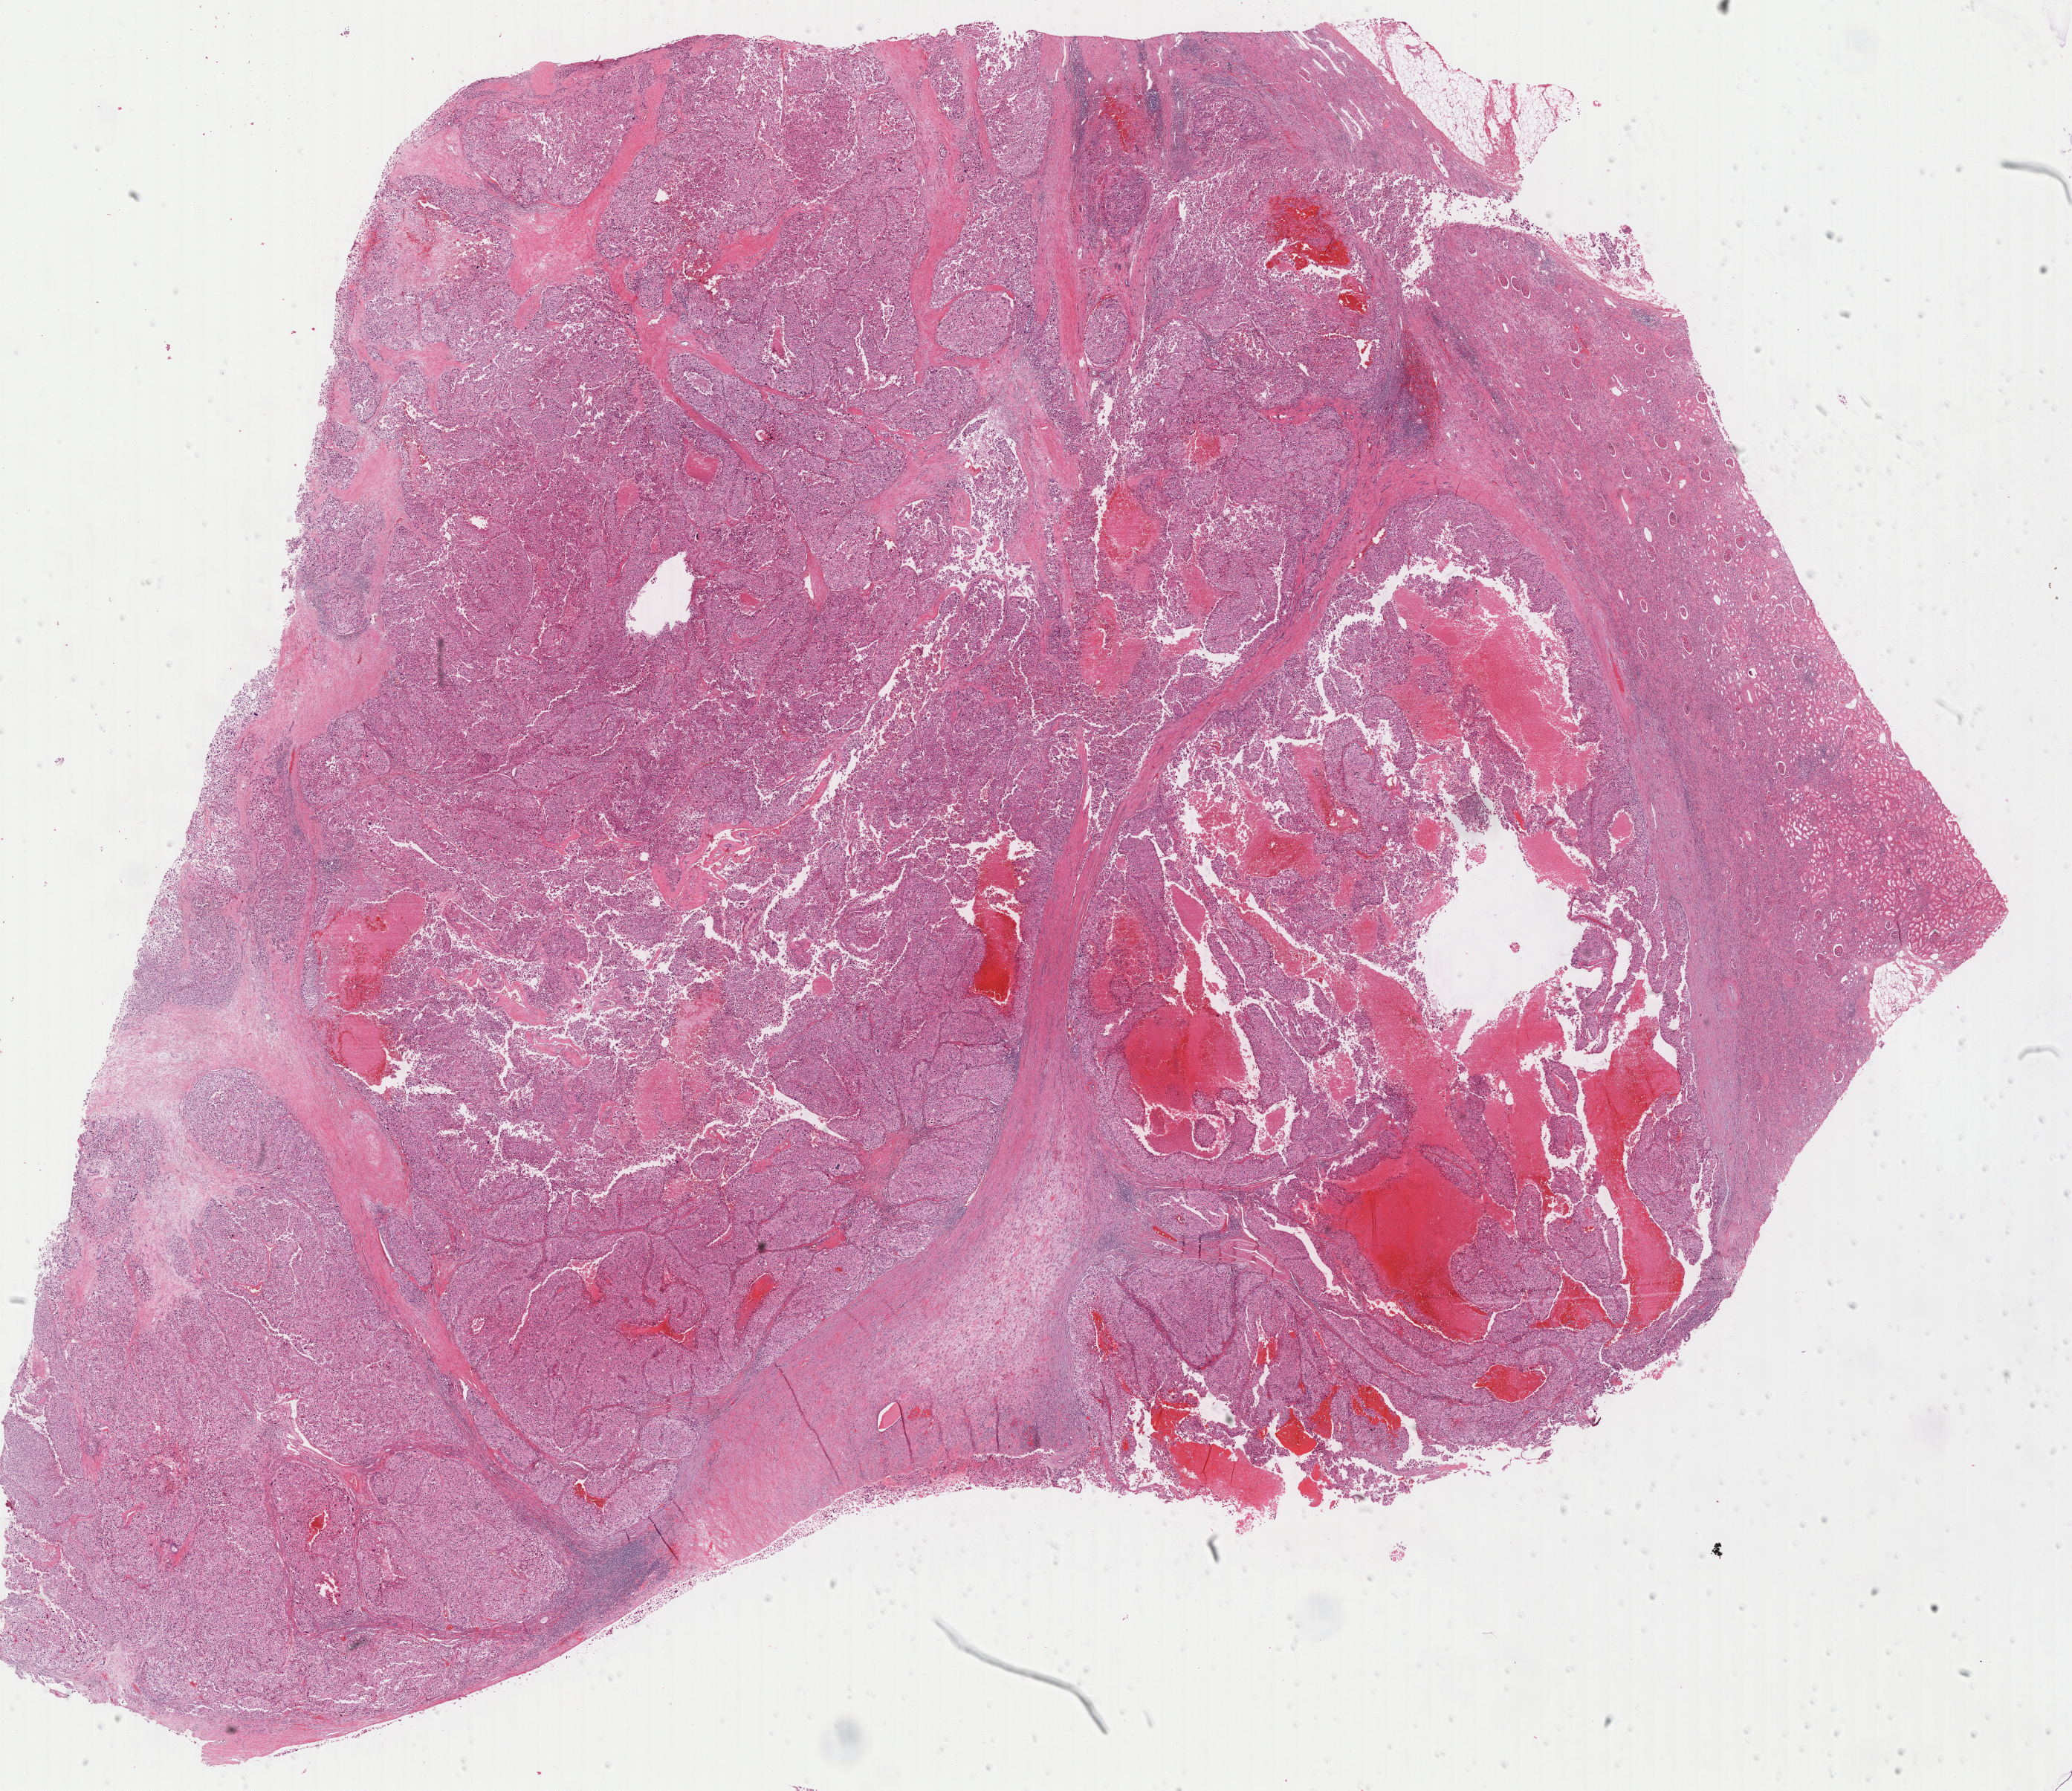
Digitized Hematoxylin and eosin (H&E) stained tissue section (whole slide), a low-resolution overview of the entire scanned area, about 22.5 x 19.4 mm (slide scanned at 40x); formalin-fixed paraffin-embedded (FFPE) diagnostic section; kidney, primary tumour sample. Patient: male, age at initial diagnosis 71 years.
TNM: T2 N0. Lymph nodes positive (case pathology): 0 of 1 examined. Histologic diagnosis: Renal cell carcinoma, chromophobe type. AJCC pathologic stage: II (6th edition).